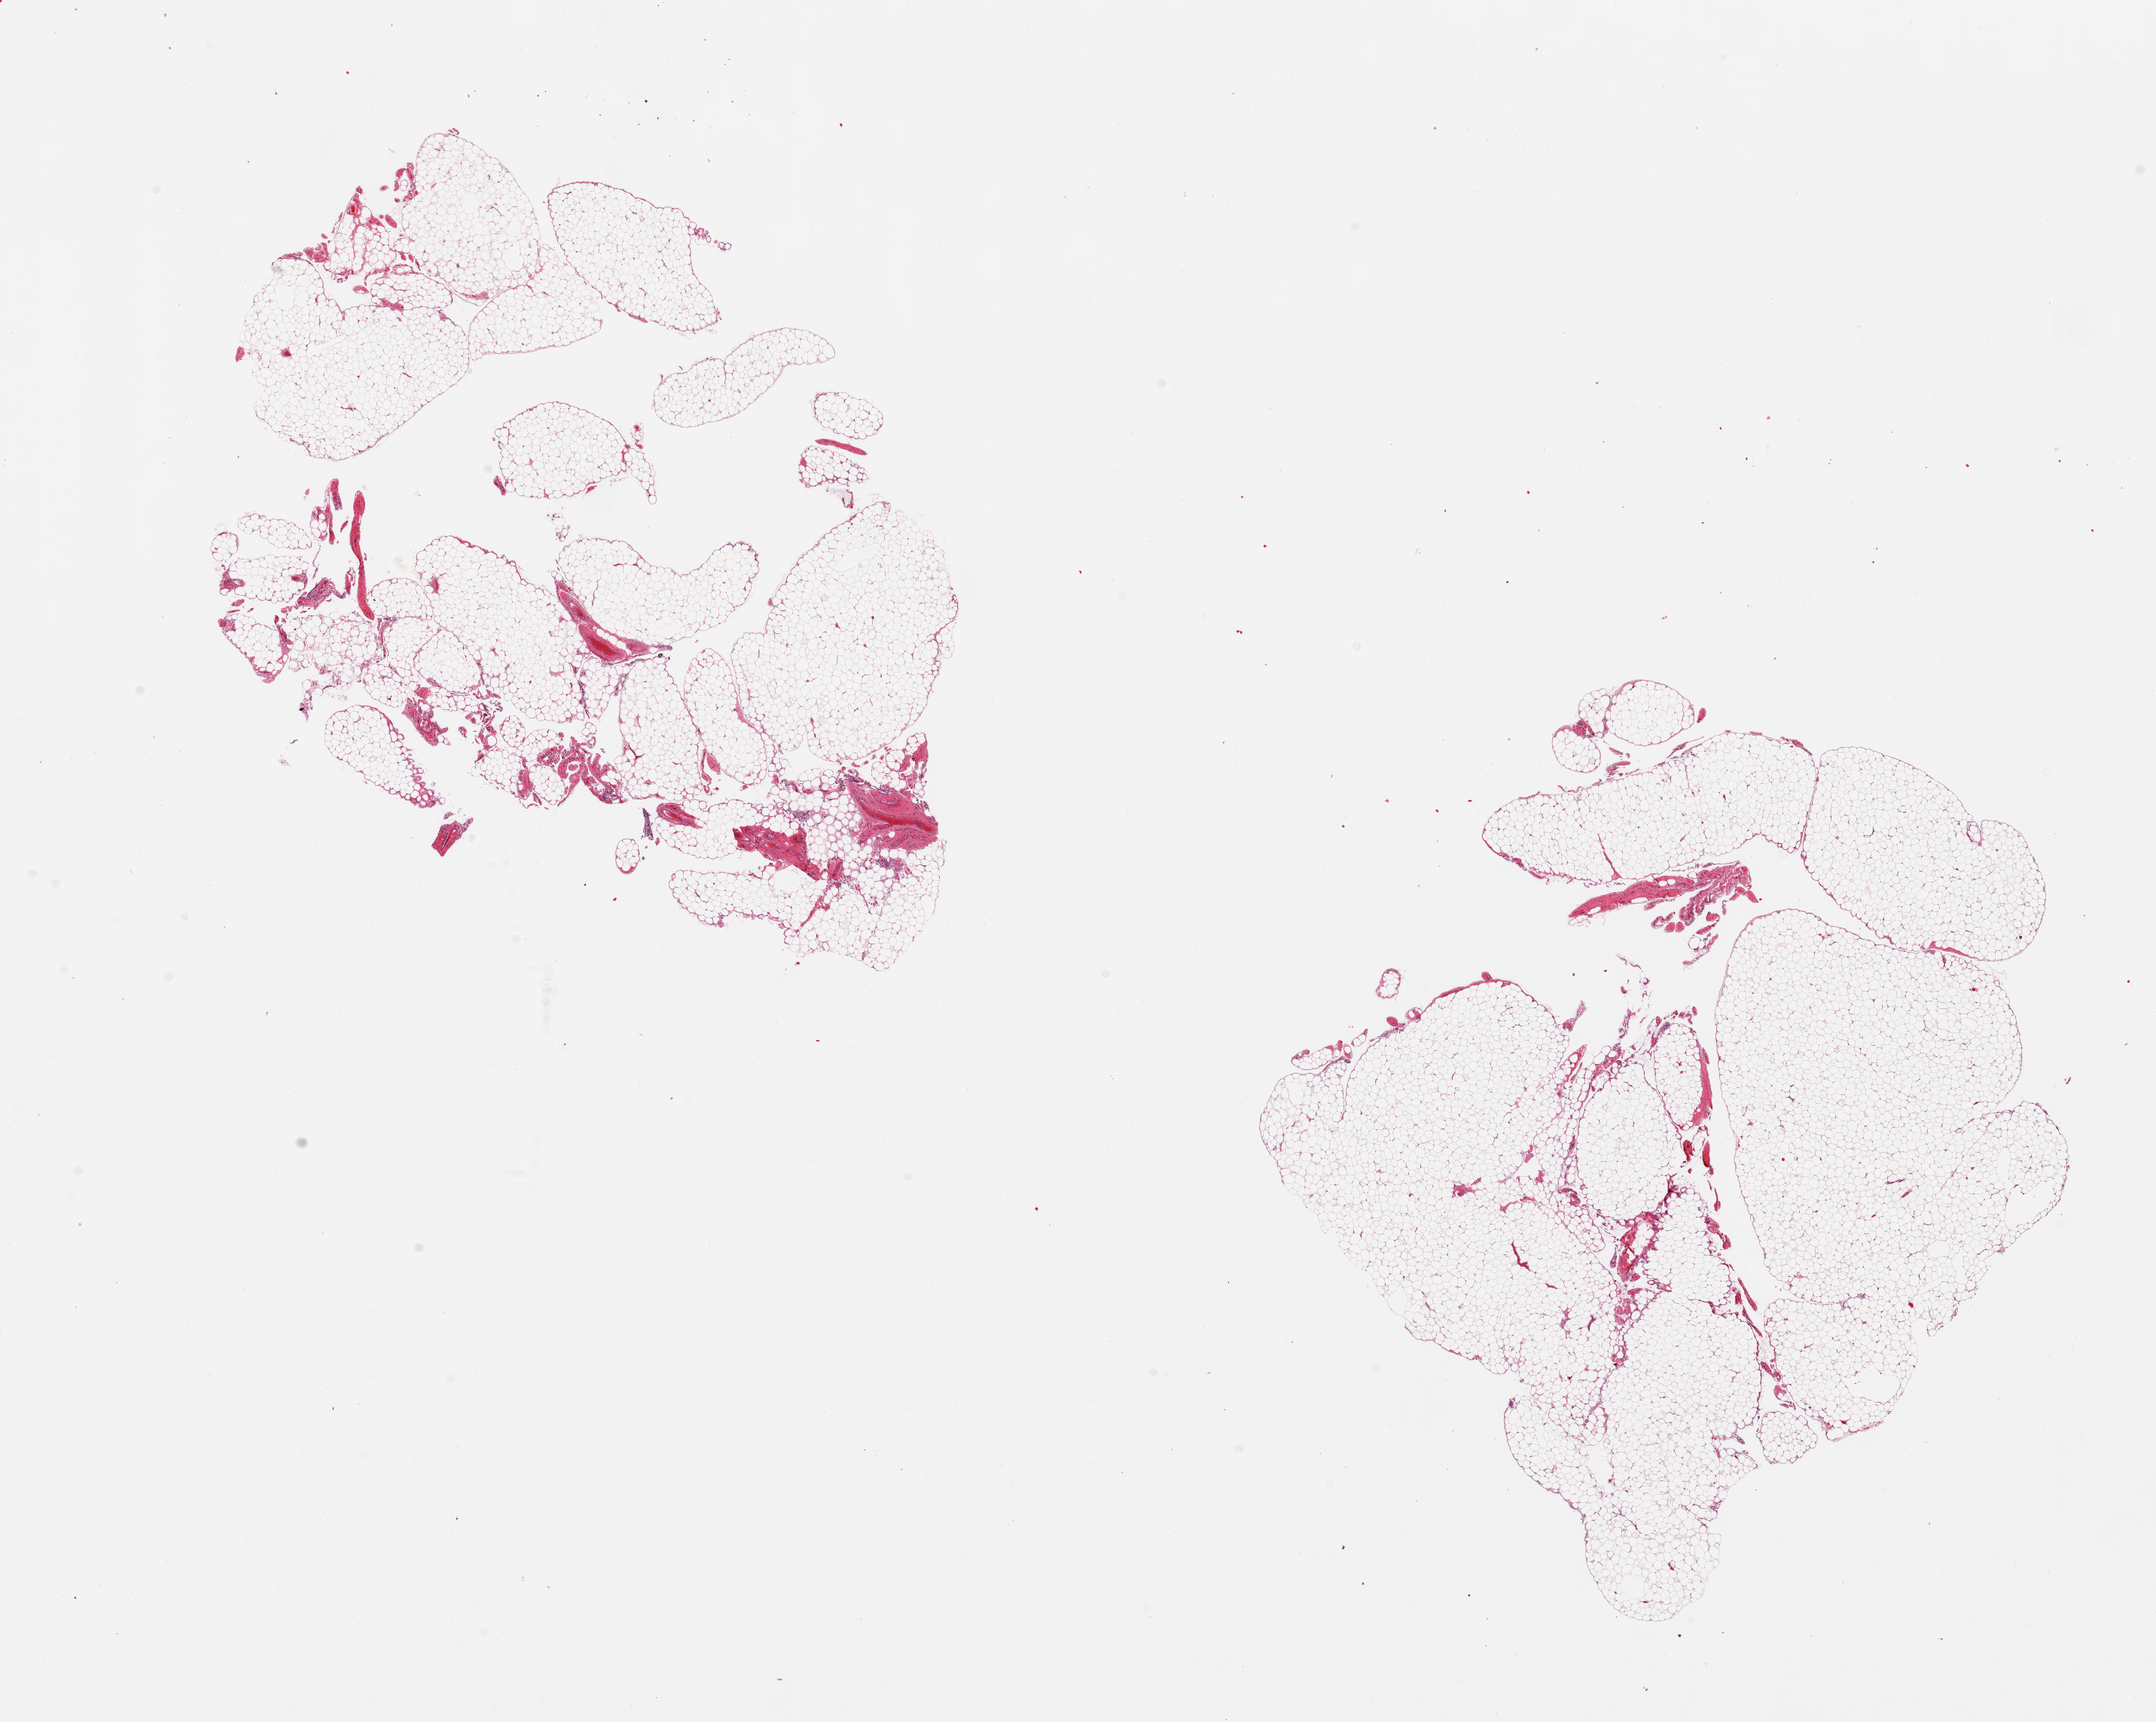
Whole-slide image, hematoxylin and eosin (H&E) stain — low-resolution overview of the scanned area, about 22.6 x 18.1 mm, PAXgene-fixed, paraffin-embedded tissue, sampled site (target tissue): omentum, tissue donor sample. Donor: female.
Pathologist's review note for this sample: 2 pieces; 5% fibrovascular content.